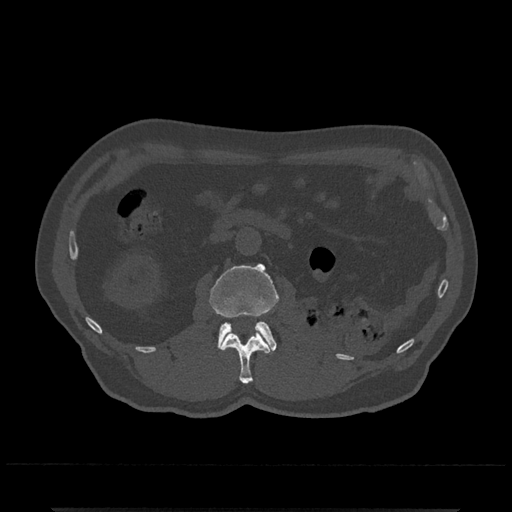
CT including the spine, one axial slice. Slice 322 of 797 in the series (ordered by position). 120 kVp. Bone window (W 1800 / L 400 HU). 0.5 mm slice thickness. 512 × 512 image matrix. Male patient, age 67 years. From the clinical record (not read from this slice): primary cancer: prostate.
Structures marked on this image (semi-automatic segmentation, software-assisted and operator-edited):
- L1 vertebra: box from (x=219, y=331) to (x=270, y=384) px
- L2 vertebra: (x=210, y=263)–(x=278, y=352)